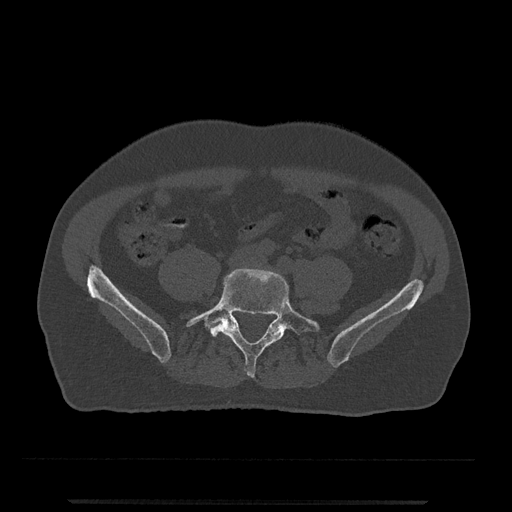
CT including the spine, one axial slice. Slice 76 of 797 in the series (ordered by position). Bone window (W 1800 / L 400 HU). 0.5 mm slice thickness. 512 × 512 image matrix. Male patient, age 63 years. From the clinical record (not read from this slice): primary cancer: prostate.
Annotated regions visible in this slice (semi-automatically segmented with operator editing):
- L5 vertebra: bounding box (x1, y1, x2, y2) in pixels: (186, 268, 320, 378)